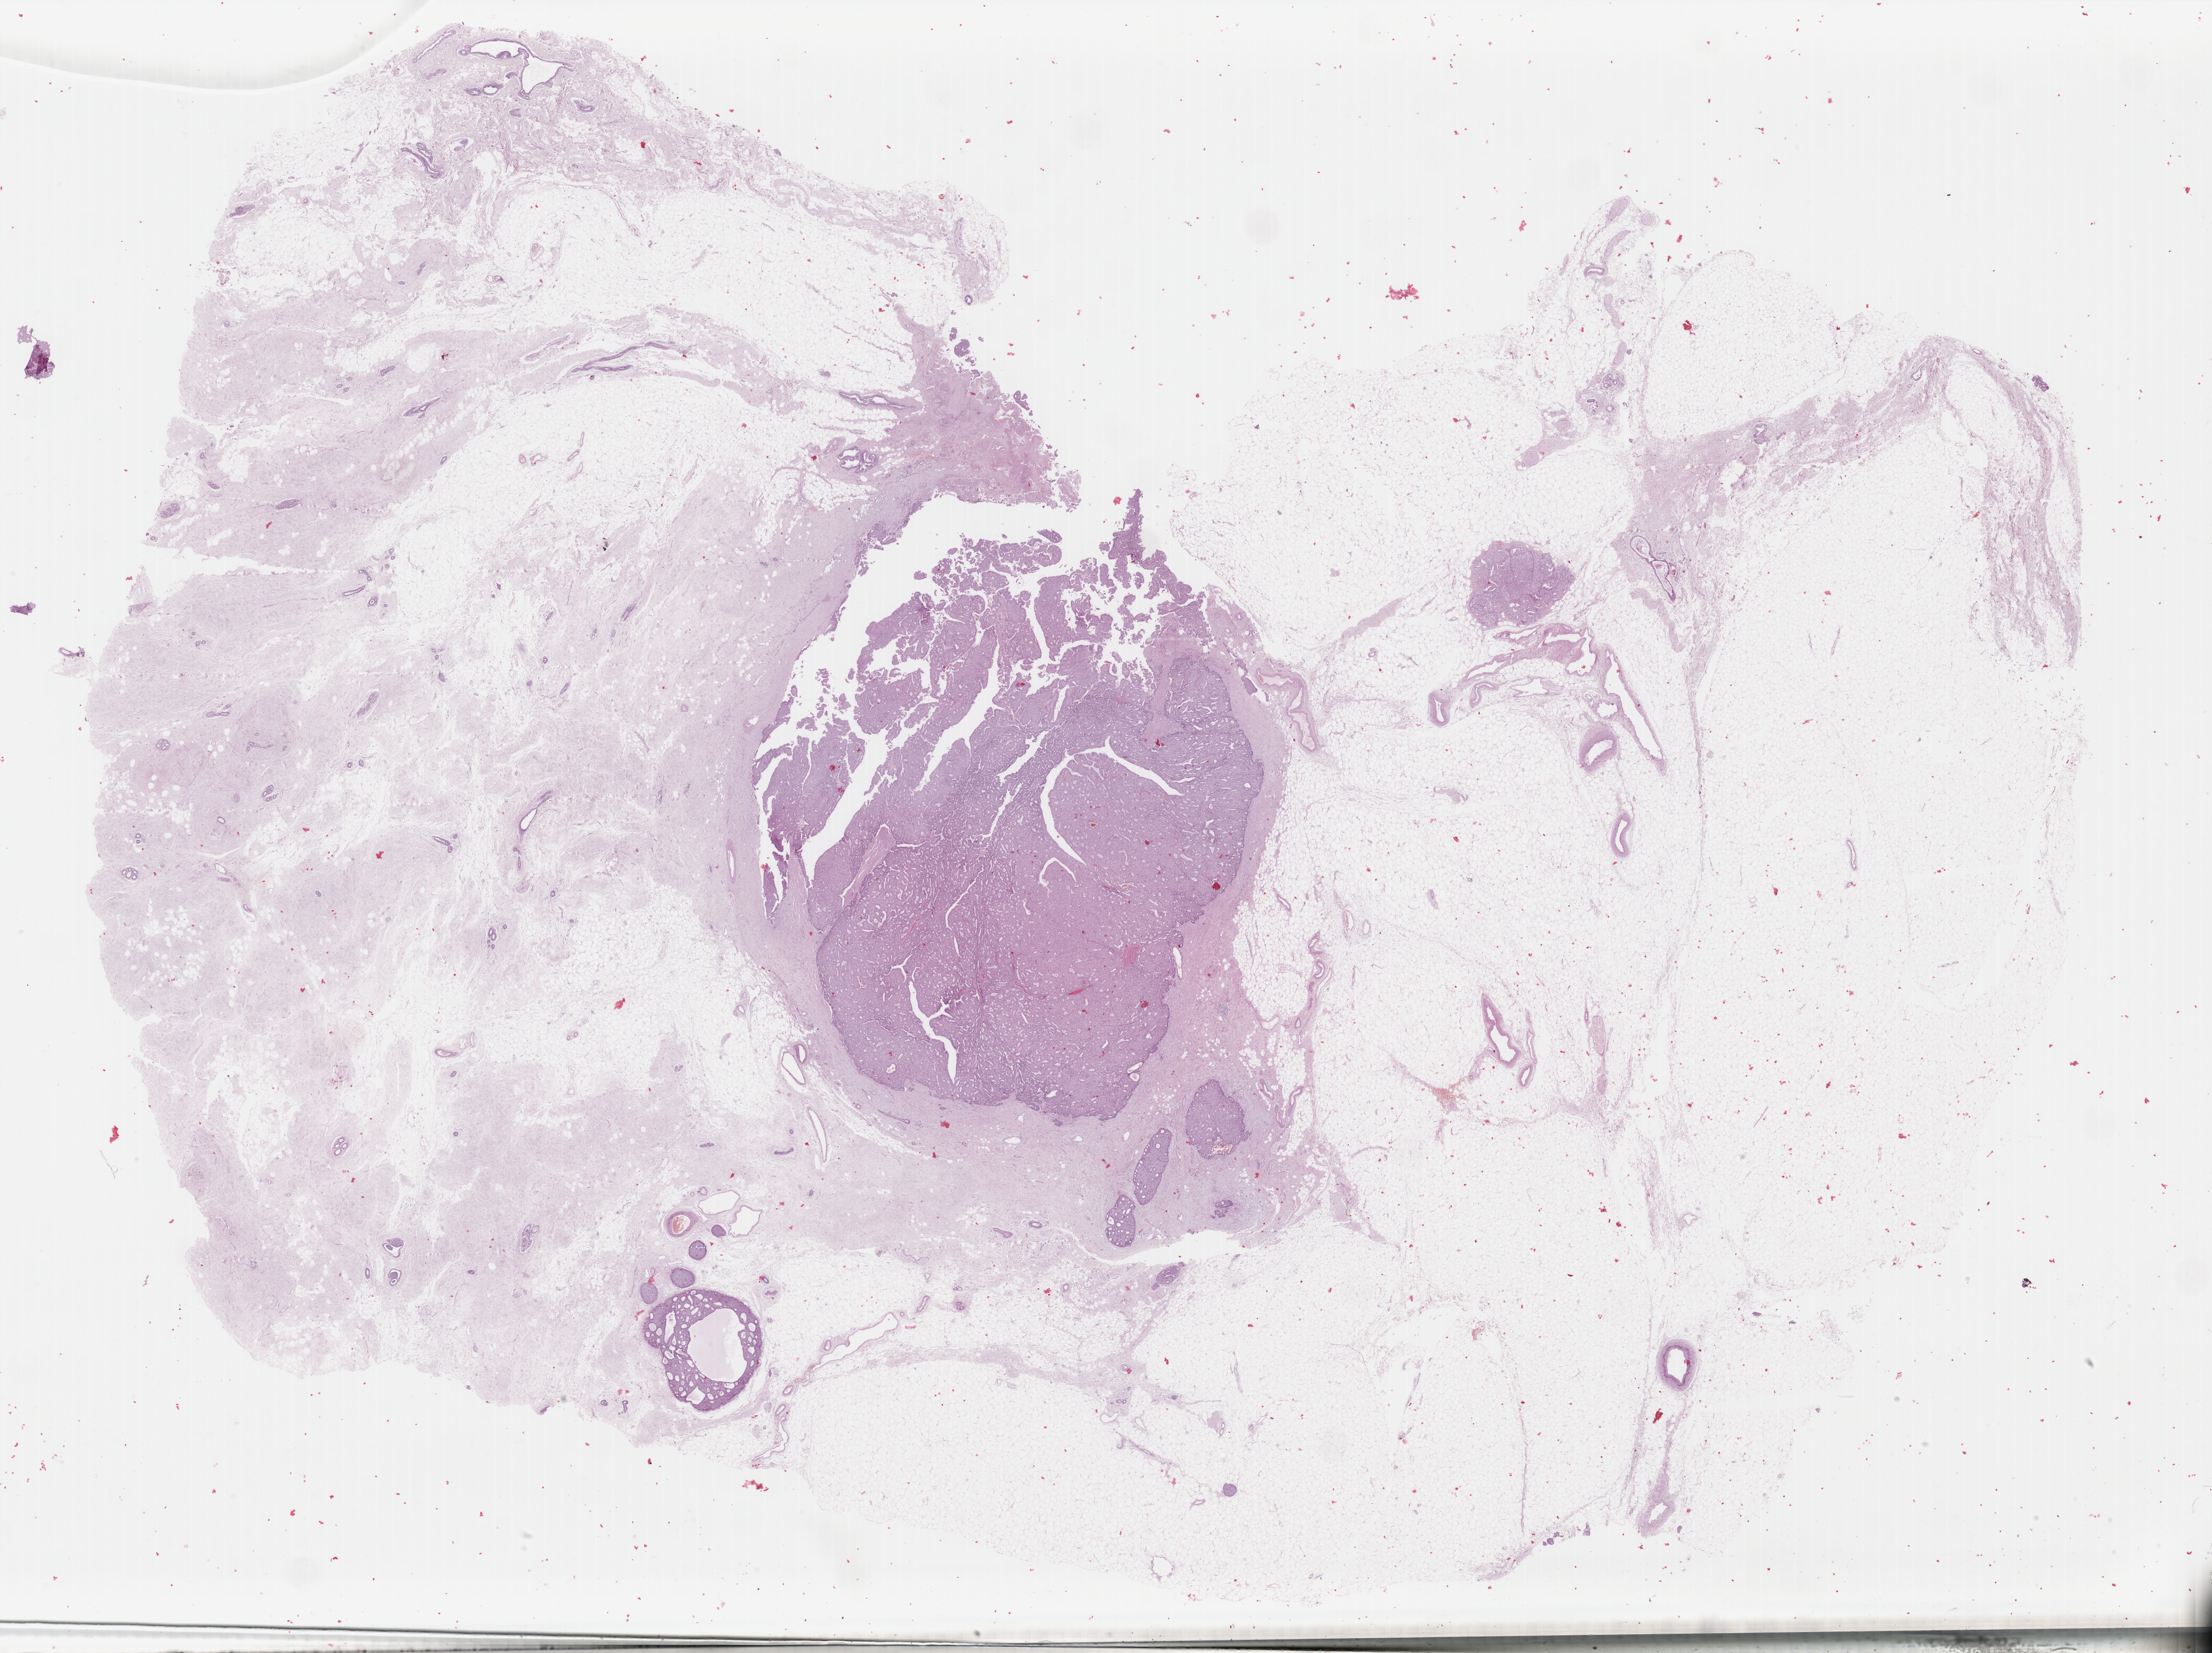
Digitized H&E tissue section (whole slide), a low-resolution overview of the entire scanned area, about 30.9 x 23.1 mm (acquisition: 40x scan). FFPE section. Breast, primary tumour sample. Patient: female, age at initial diagnosis 77 years.
• TNM: T1c N0 M0
• histologic diagnosis: Intraductal papillary adenocarcinoma with invasion
• AJCC pathologic stage: IA (7th edition)